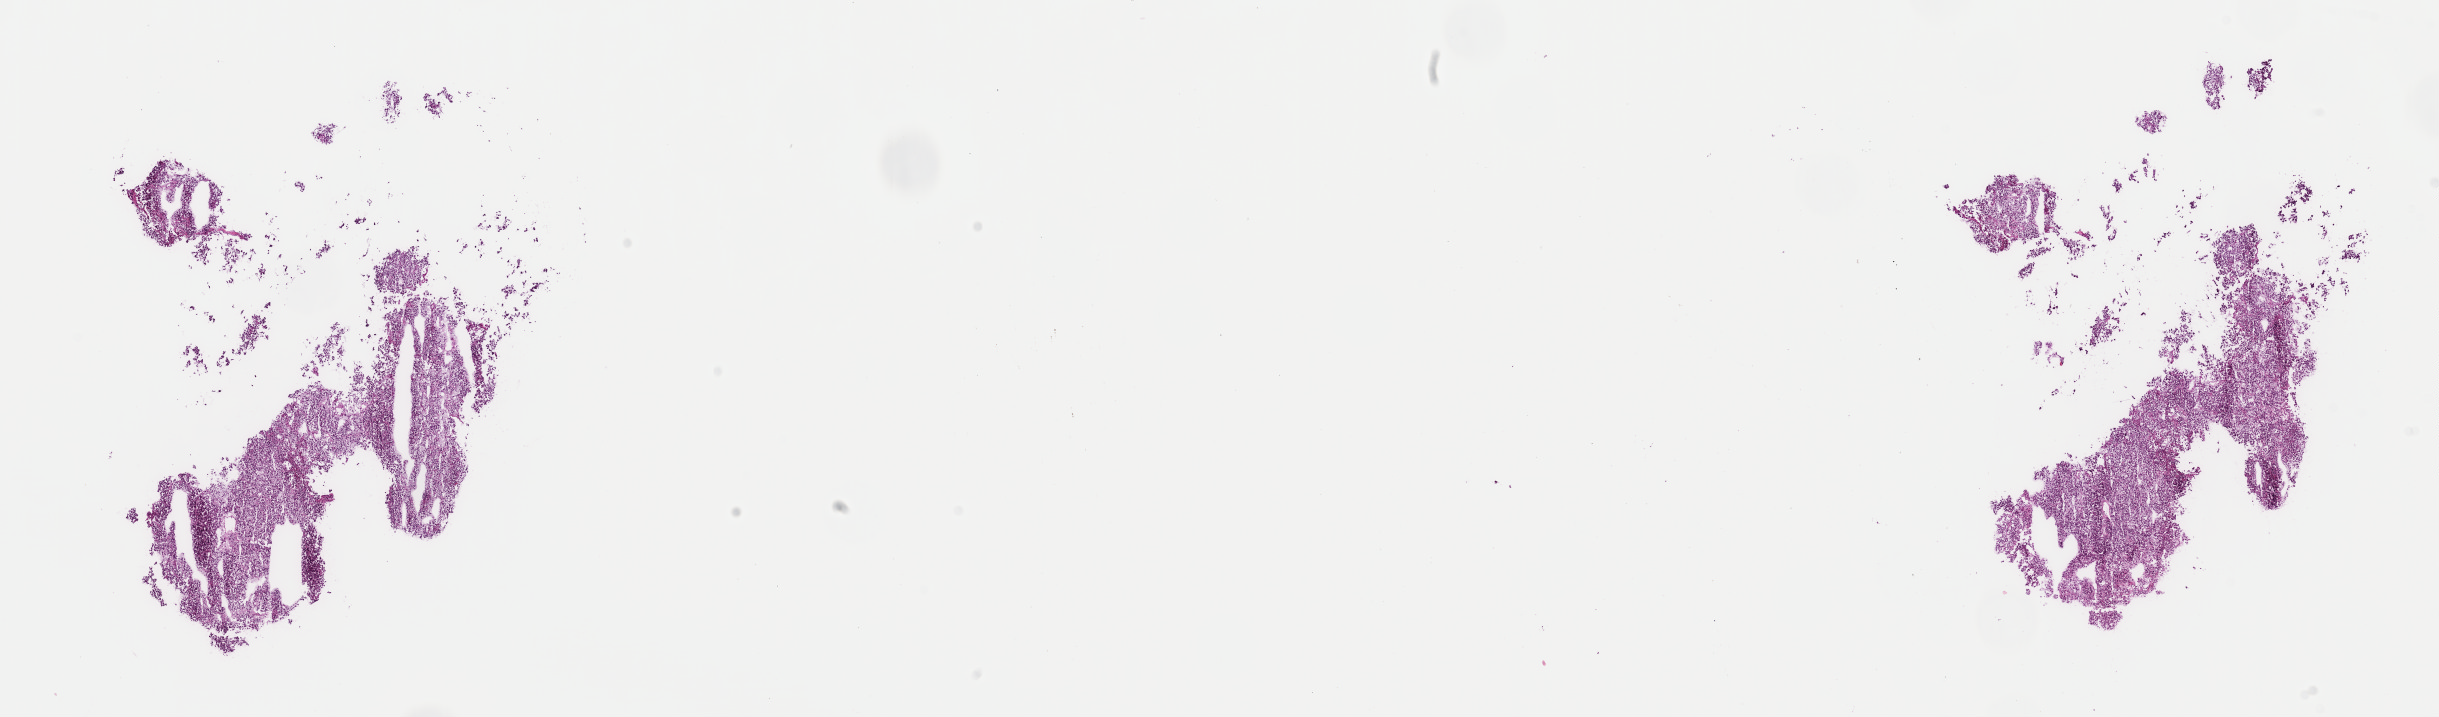
H&E-stained whole-slide image — shown as a low-resolution overview of the whole scanned area (about 19.3 x 5.7 mm, from a 40x scan). Frozen section from the top of the tissue portion. Adrenal gland, primary tumour sample. Female patient; age at initial diagnosis 31 years. Slide review estimates, as recorded: tumour cells 100%, tumour nuclei 95%, normal cells 0%, stromal cells 0%, necrosis 0%. Inflammatory infiltration, as recorded: lymphocyte infiltration 0%, monocyte infiltration 0%, neutrophil infiltration 0%.
* diagnosis: Pheochromocytoma, NOS
* laterality: right